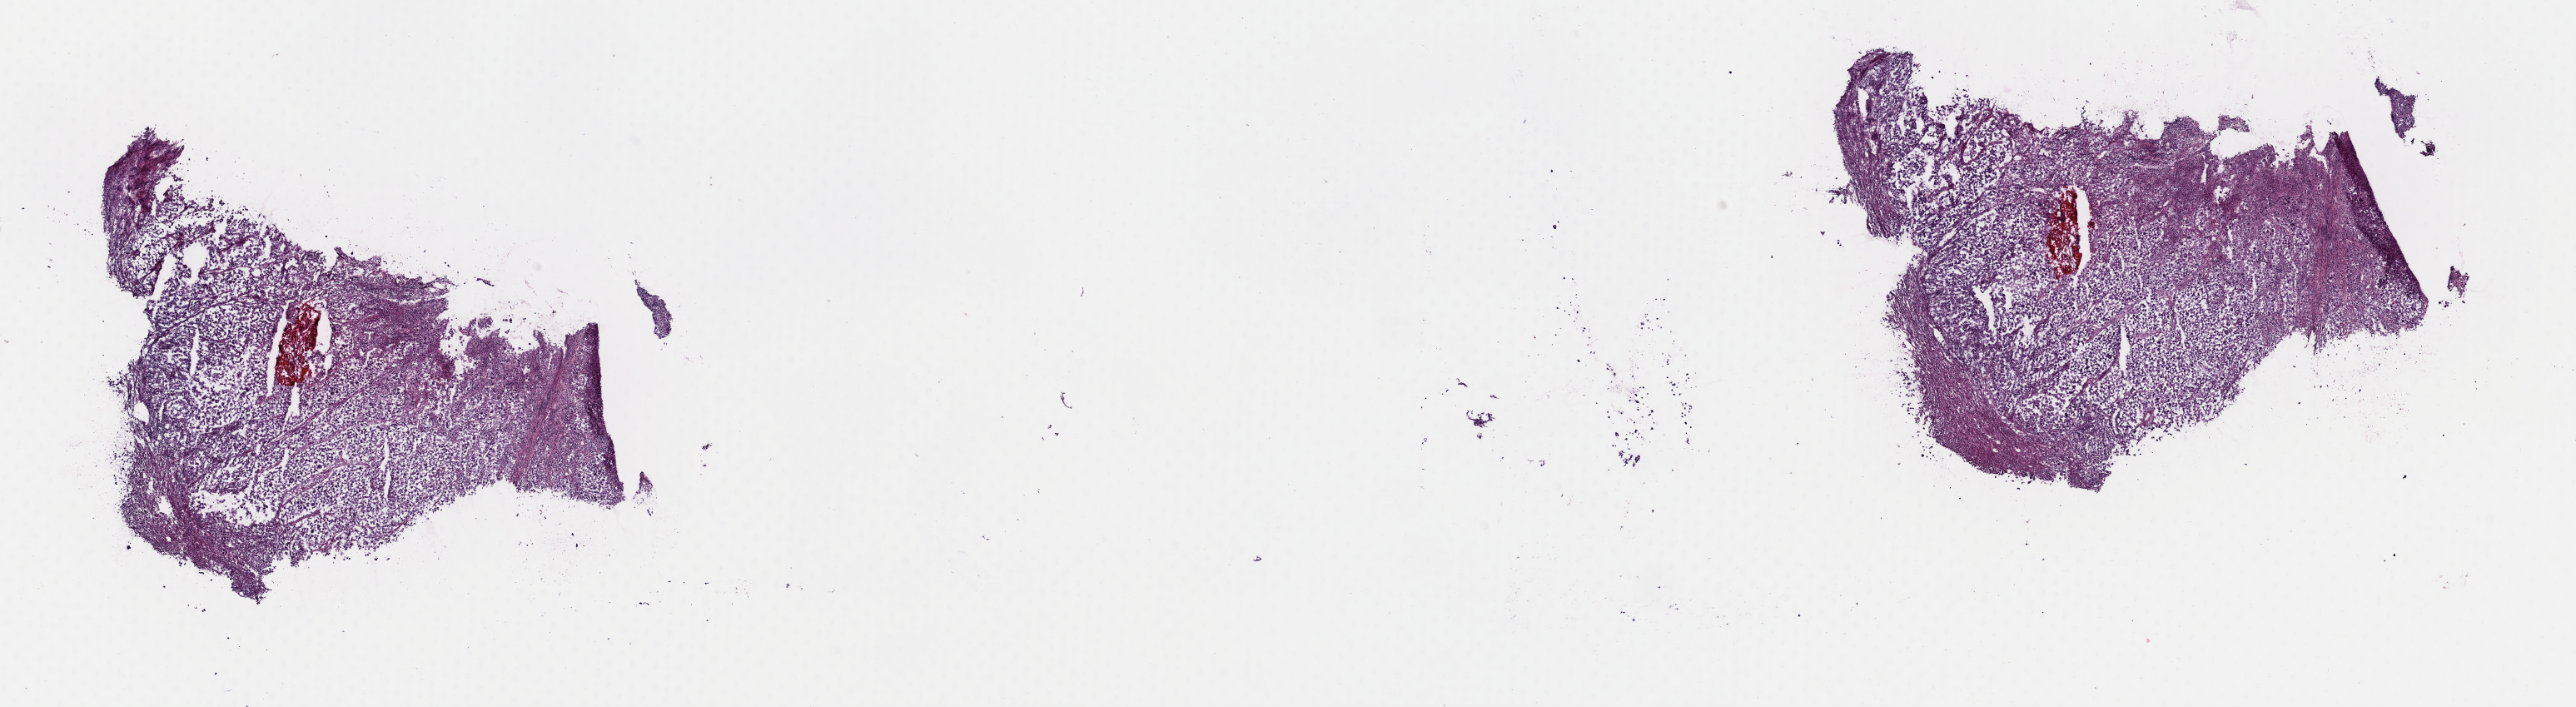
Whole-slide histology image, H&E — shown as a low-resolution overview of the whole scanned area (about 24.4 x 6.7 mm). Frozen section from the top of the tissue portion. Metastatic tumour sample, sampled site: adrenal gland. Patient: male, age at initial diagnosis 49 years. Composition of this section per pathologist review: tumour cells 100%, tumour nuclei 80%, normal cells 0%, stromal cells 0%, necrosis 0%. Infiltration values recorded for this section: lymphocyte infiltration 0%, monocyte infiltration 0%, neutrophil infiltration 0%.
This section: metastatic tumour tissue. Patient diagnosis: Malignant melanoma, NOS.